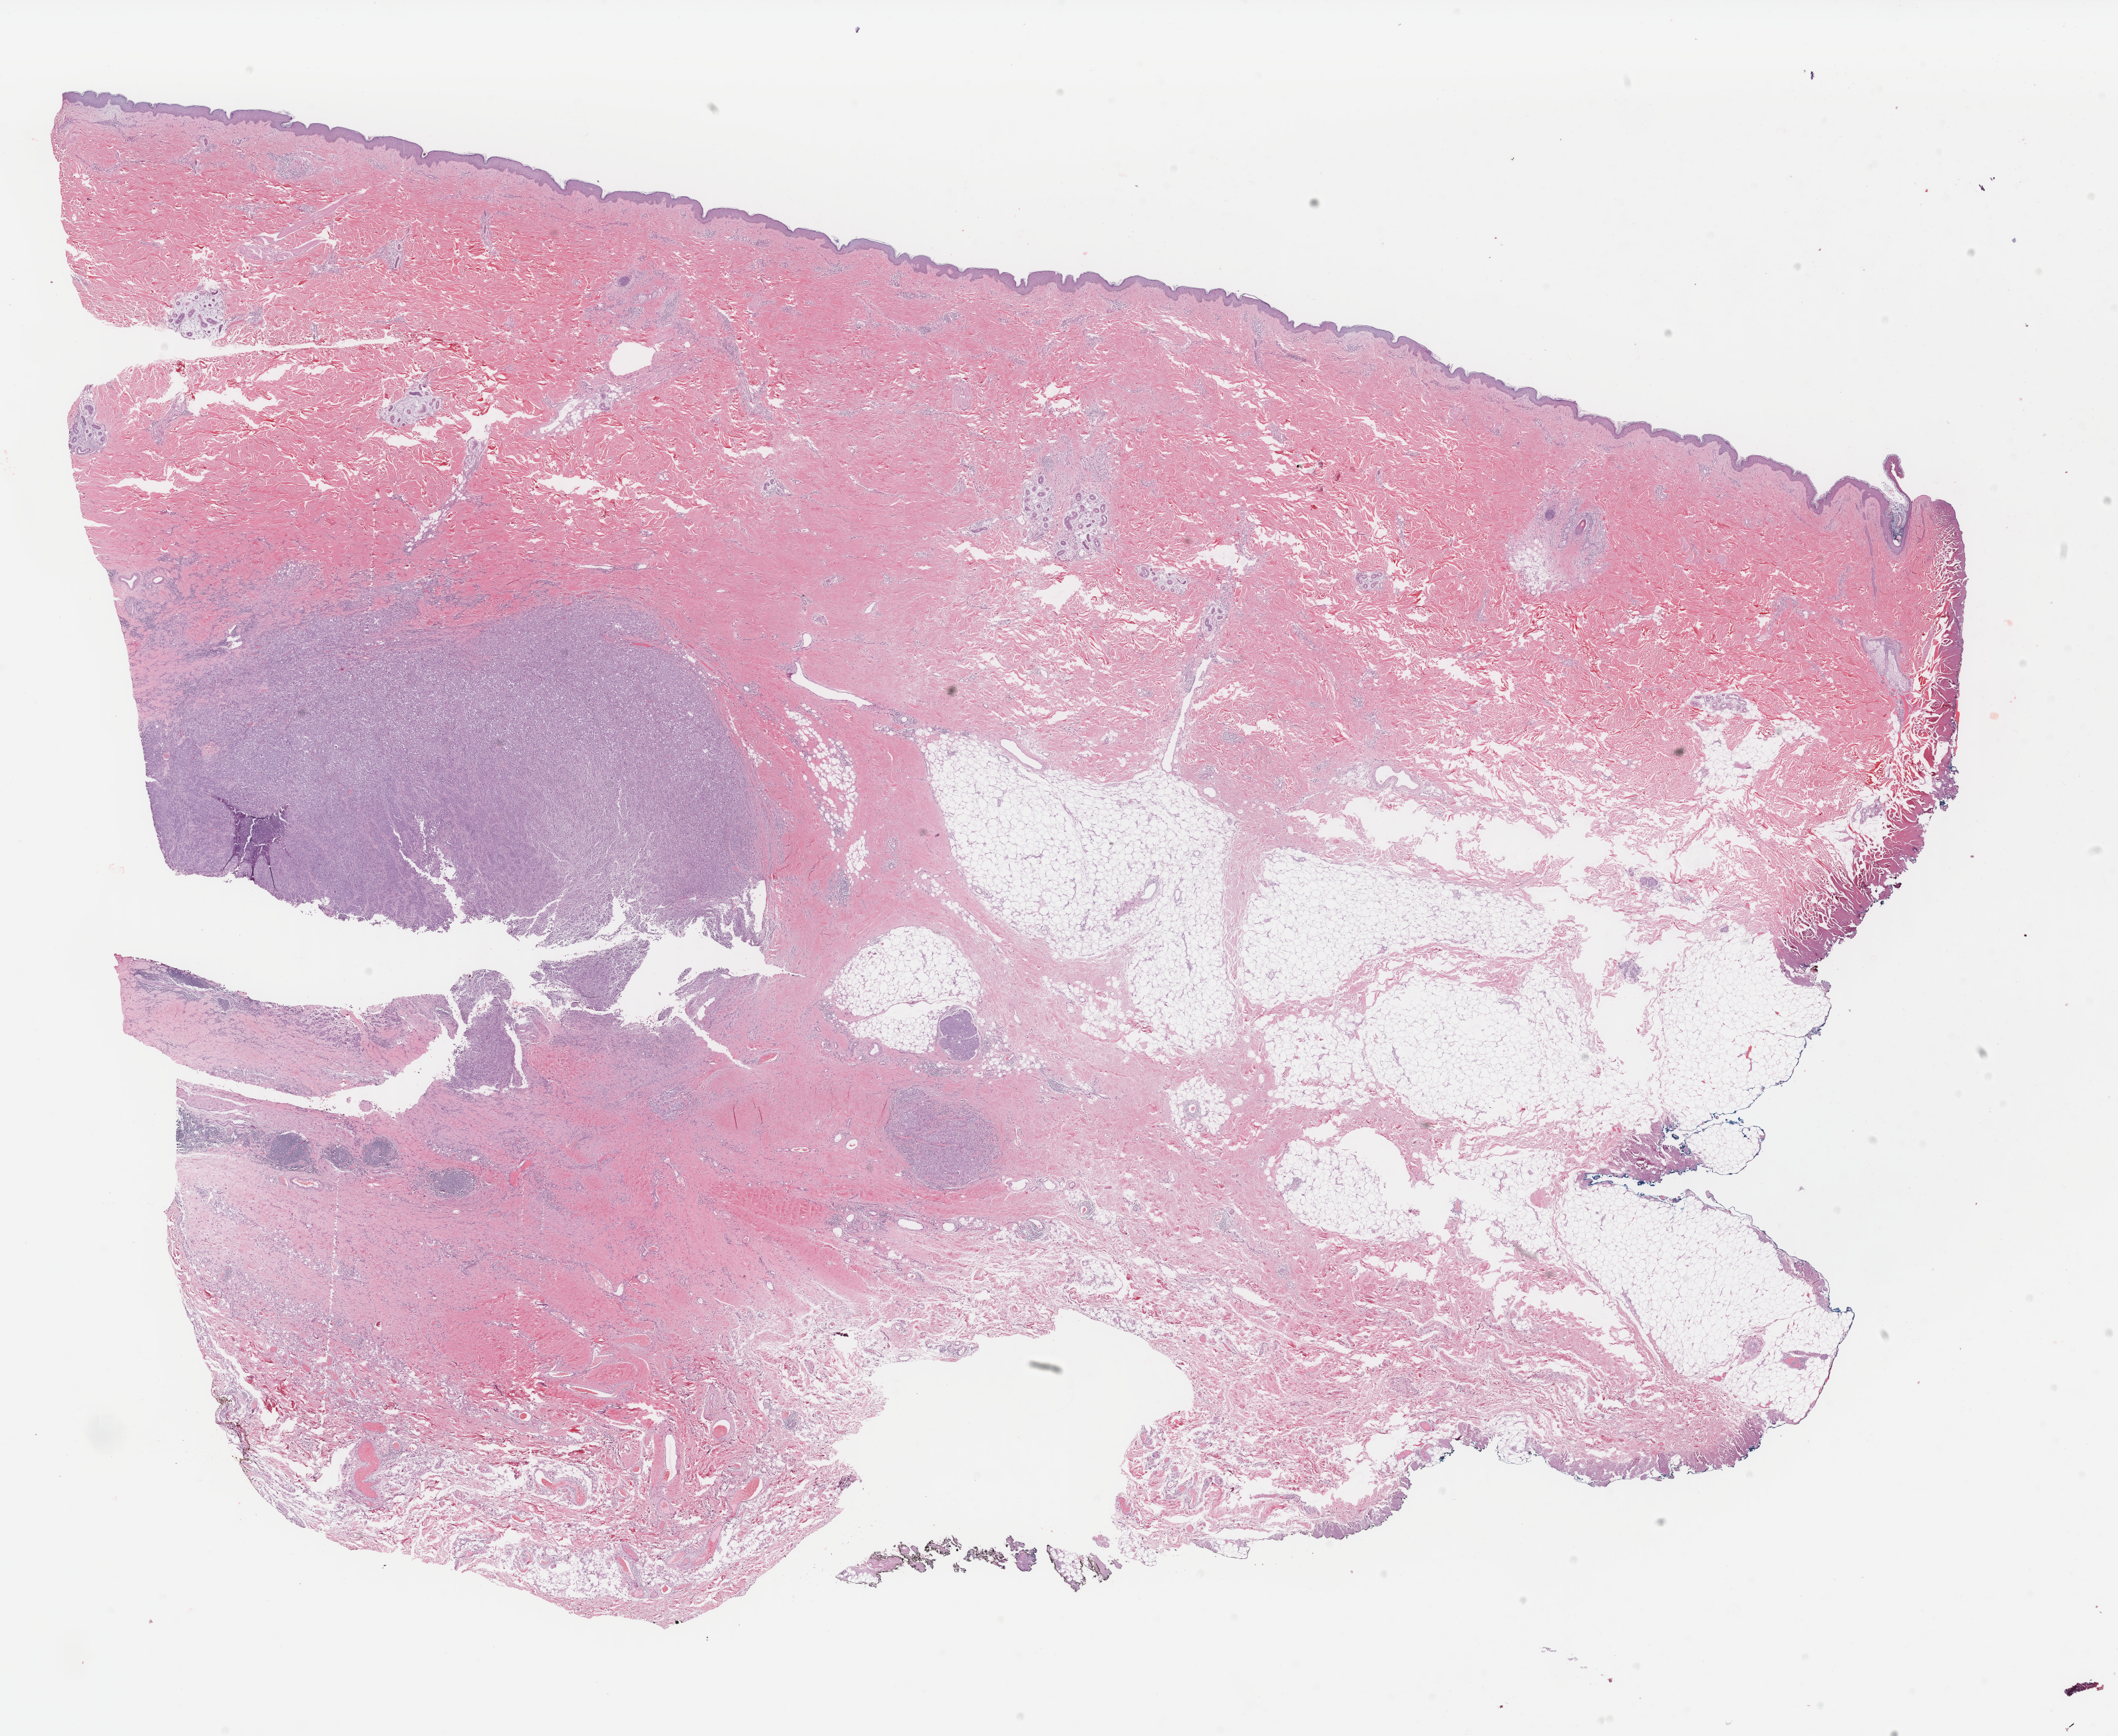
Digitized H&E-stained tissue section (whole slide), shown as a low-resolution overview of the whole scanned area (about 25.3 x 20.7 mm, from a 40x scan), FFPE section, metastatic tumour sample, sampled site not recorded. Patient: female, age at initial diagnosis 63 years.
This section: metastatic tumour tissue. Patient diagnosis: Malignant melanoma, NOS.